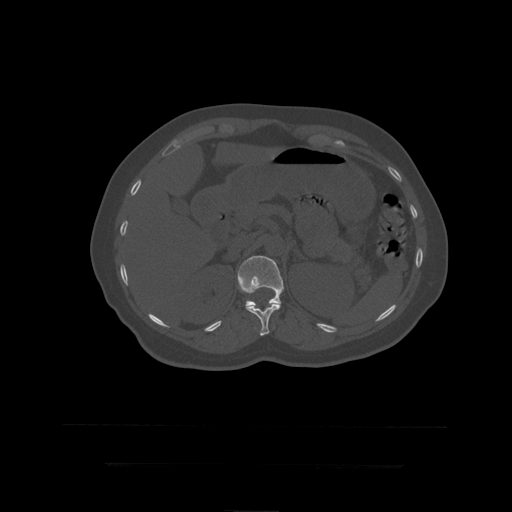
CT including the spine, one axial slice; position 186 of 399 along the scan axis; reconstruction kernel STANDARD; 120 kVp; bone window (W 1800 / L 400 HU); 1.25 mm slice thickness; 512 × 512 image matrix, field of view 450 × 450 mm. Patient age 41 years. From the clinical record (not read from this slice): primary cancer: breast.
Structures marked on this image (semi-automatic segmentation, software-assisted and operator-edited):
- L1 vertebra: bounding box (x1, y1, x2, y2) in pixels: (238, 256, 285, 307)
- T12 vertebra: (246, 303, 281, 336)